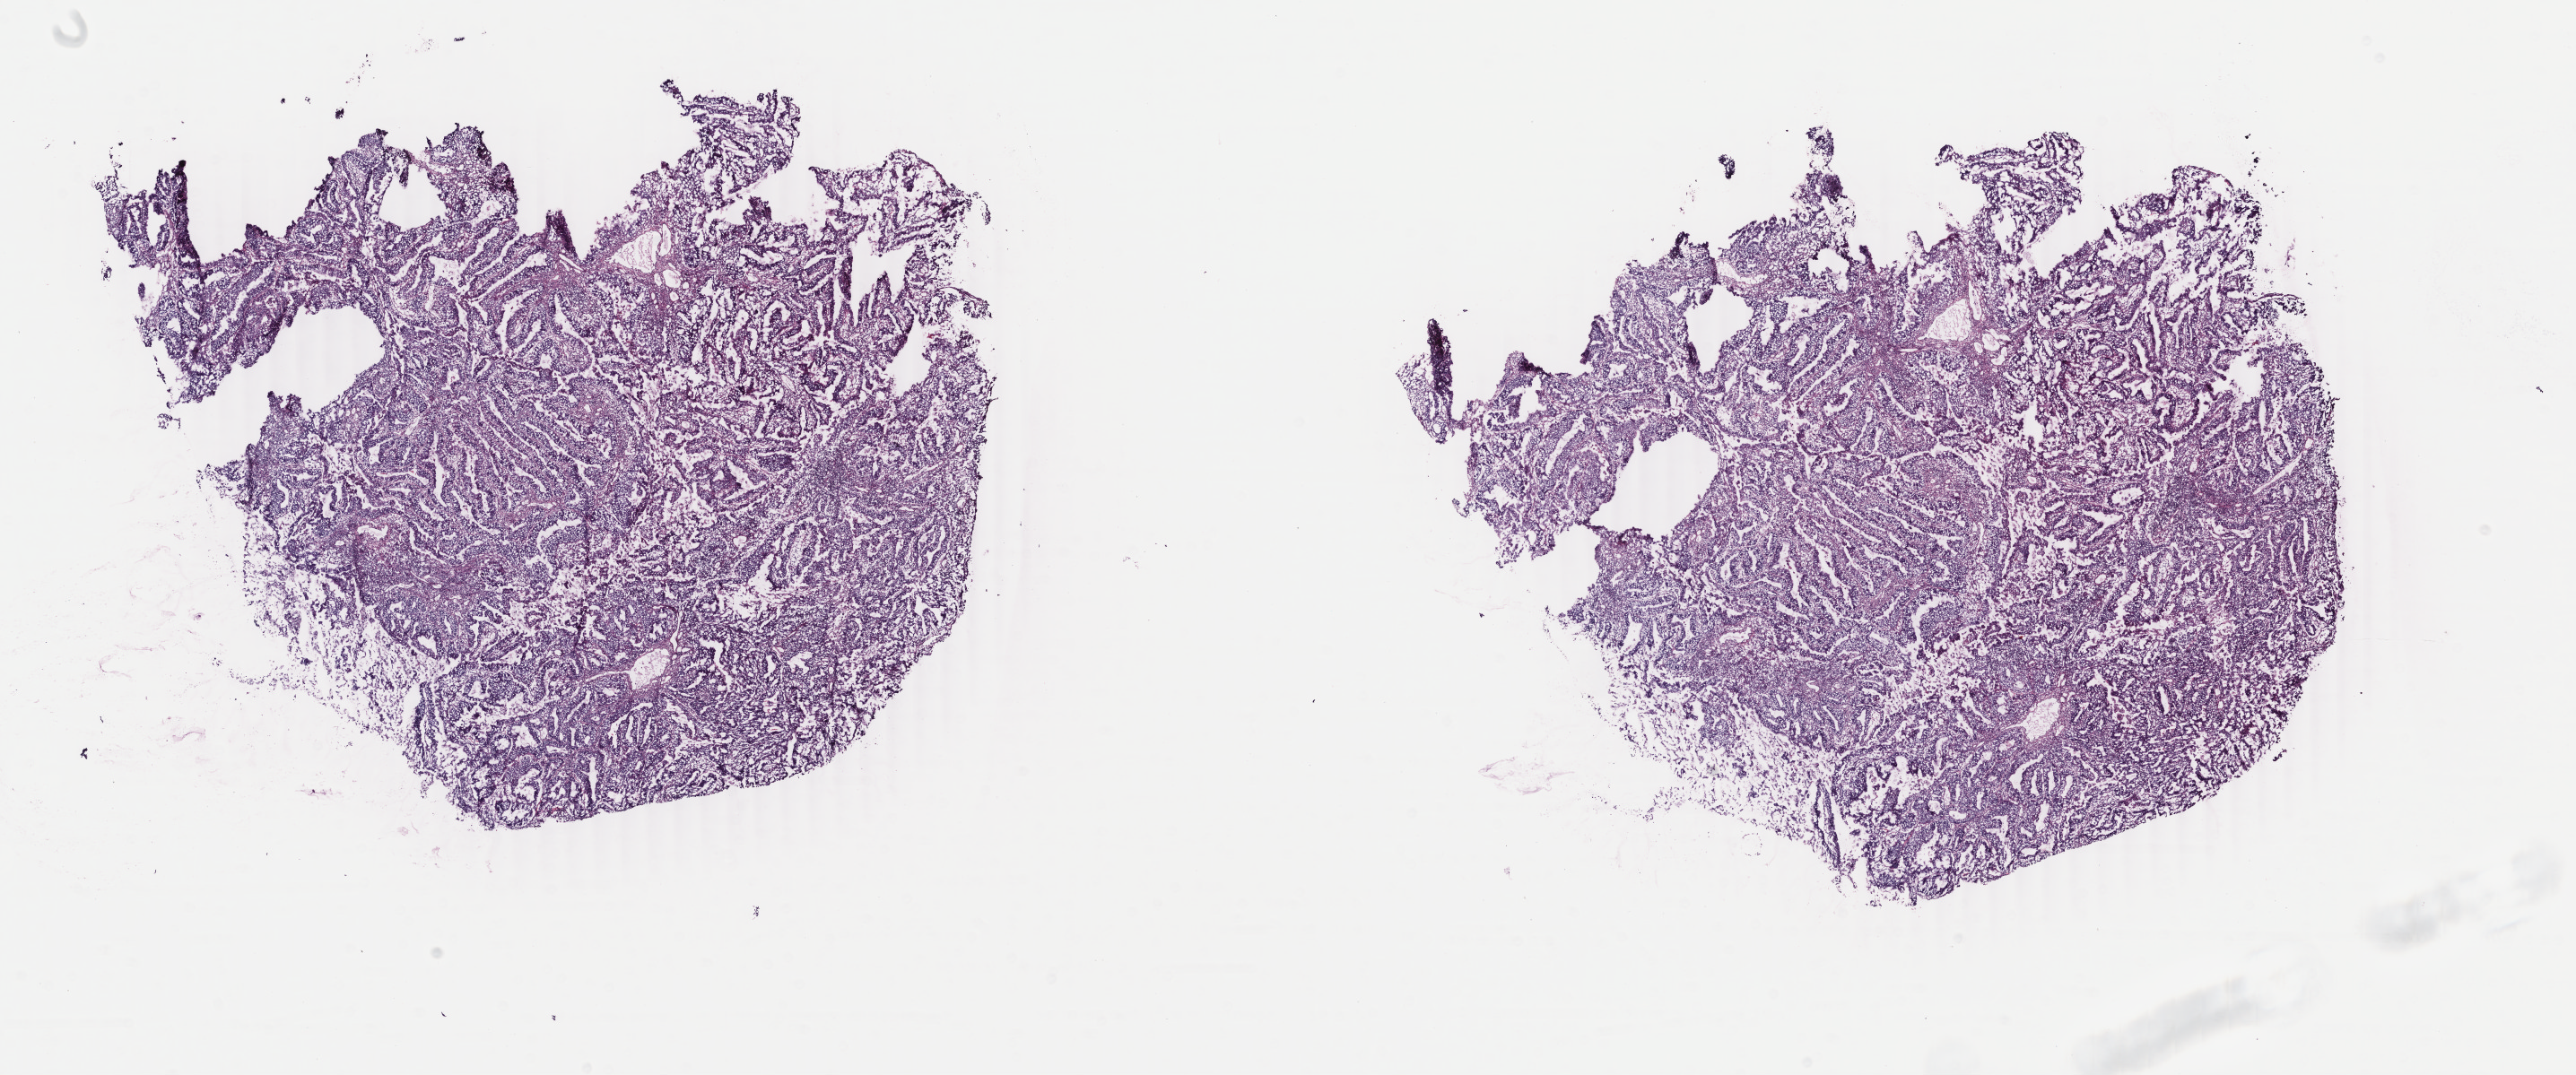
Whole-slide histology image, H&E-stained — shown as a low-resolution overview of the whole scanned area (about 22.8 x 9.5 mm). Frozen section from the bottom of the tissue portion. Primary tumour sample from the uterus. Patient: female, age at initial diagnosis 55 years. Histologic grade: G2 (moderately differentiated). Slide review estimates, as recorded: tumour cells 70%, tumour nuclei 70%, normal cells 0%, stromal cells 30%, necrosis 0%. Infiltration values recorded for this section: lymphocyte infiltration 40%, monocyte infiltration 10%, neutrophil infiltration 20%.
- FIGO stage: IA
- diagnosis: Endometrioid adenocarcinoma, NOS (endometrium)